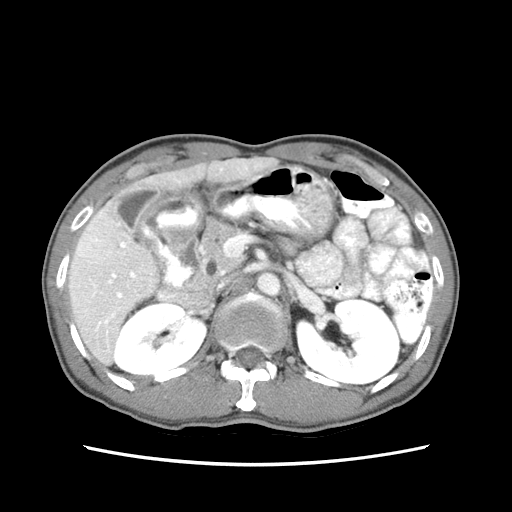
Contrast-enhanced abdominal CT (liver protocol), one axial slice; position 31 of 79 along the scan axis; reconstruction kernel STANDARD; 120 kVp; soft-tissue window (W 400 / L 40 HU); 512 × 512 image matrix. Case-level facts recorded for this patient, not image findings: diagnosis: hepatocellular carcinoma (patient treated with transarterial chemoembolisation; whether this scan precedes or follows treatment is not stated here); TNM stage (as recorded): Stage-IIIB; Child-Pugh class: A; tumour differentiation: moderately differentiated; tumour nodularity: multinodular.
Annotated regions visible in this slice (semi-automatically segmented with operator editing):
- liver parenchyma outside the tumour (the mass and vessels are separate outlines, so this box may not span the whole liver): bounding box <68,154,278,363> (left, top, right, bottom; pixels)
- liver vessels: <79,165,248,348>